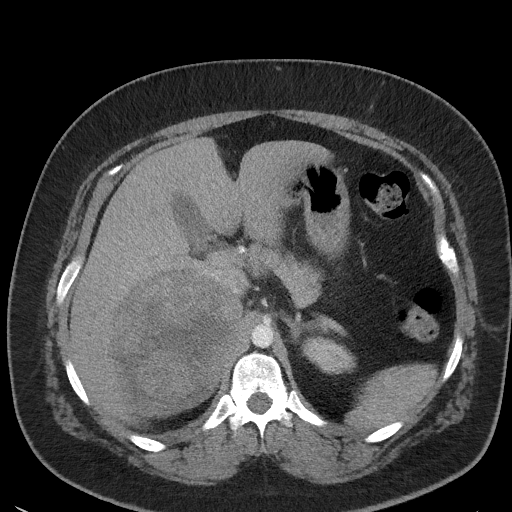
Contrast-enhanced abdominal CT, one axial slice; reconstruction kernel I41f/3; 120 kVp; intravenous contrast given; soft-tissue window (W 400 / L 40 HU); 512 × 512 image matrix, field of view 373 × 373 mm. Female patient, age 35 years. From the clinical record (not read from this slice): diagnosis: adrenocortical carcinoma; tumour side: right adrenal; tumour size at pathology: 15 cm; Ki-67 index: 40 %; stage (as recorded): 2.
Structures marked on this image (semi-automatic segmentation, software-assisted and operator-edited):
- mass: bounding box (x1, y1, x2, y2) in pixels: (111, 272, 235, 411)